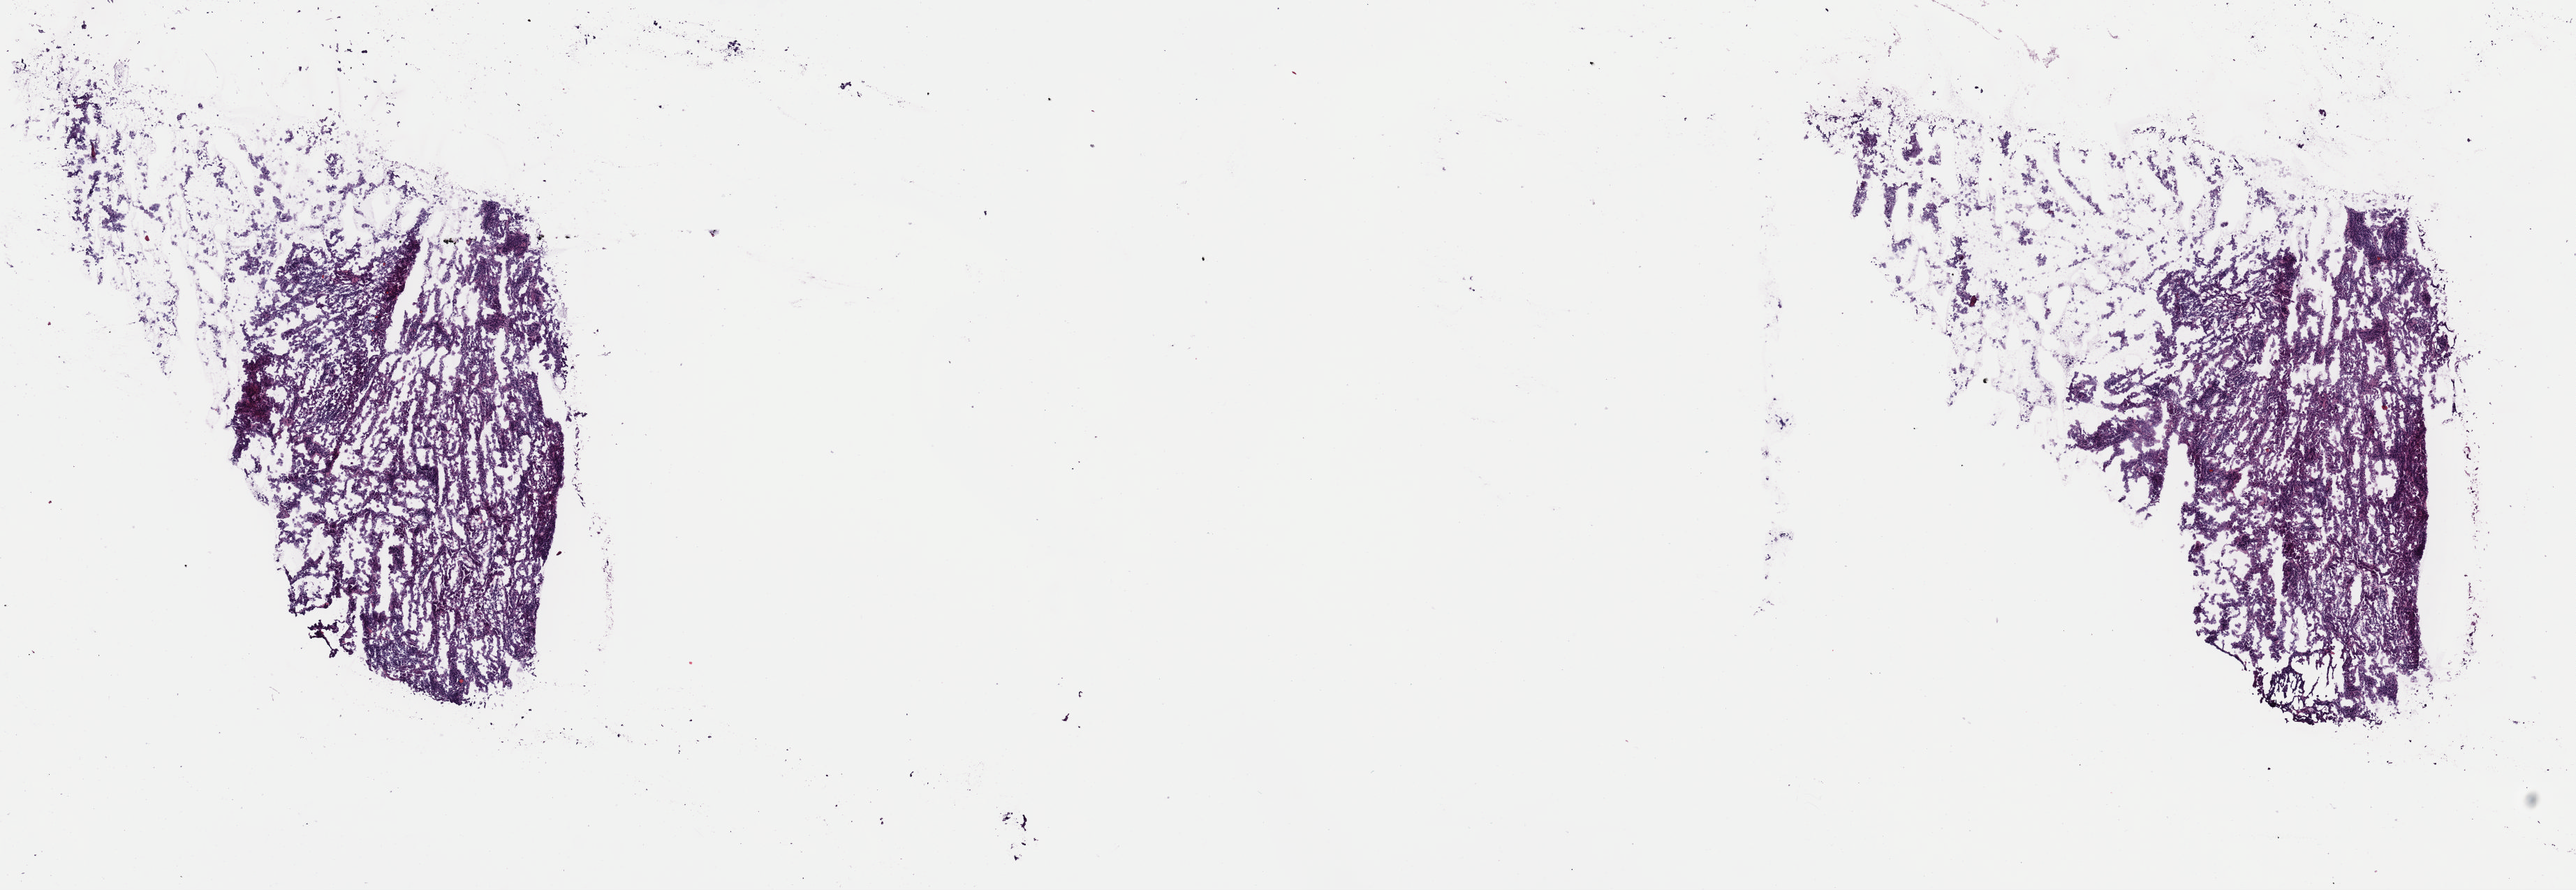
Whole-slide histology image, H&E — shown as a low-resolution overview of the whole scanned area (about 14.6 x 5.0 mm, slide scanned at 40x). Frozen section from the top of the tissue portion. Primary tumour sample from the thyroid. Female, age 31 years at initial diagnosis. Pathologist review of this section (percent, as recorded): tumour cells 100%, tumour nuclei 80%, normal cells 0%, stromal cells 0%, necrosis 0%. Inflammatory infiltration, as recorded: lymphocyte infiltration 5%, monocyte infiltration 0%, neutrophil infiltration 0%.
• lymph nodes positive (case pathology): 0 of 1 examined
• AJCC pathologic stage: I
• histologic diagnosis: Papillary adenocarcinoma, NOS (thyroid gland)
• TNM: T3 N0 MX